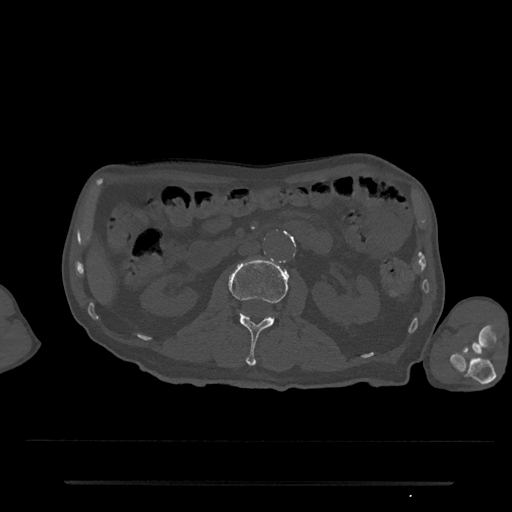
CT including the spine, one axial slice. Position 46 of 797 along the scan axis. Reconstruction kernel Br40s/3. Bone window (W 1800 / L 400 HU). 0.5 mm slice thickness. 512 × 512 image matrix, field of view 427 × 427 mm. Patient: male, 74 years. Case-level facts recorded for this patient, not image findings: primary cancer: prostate.
Annotated regions visible in this slice (semi-automatically segmented with operator editing):
- L2 vertebra: box from (x=229, y=258) to (x=289, y=366) px